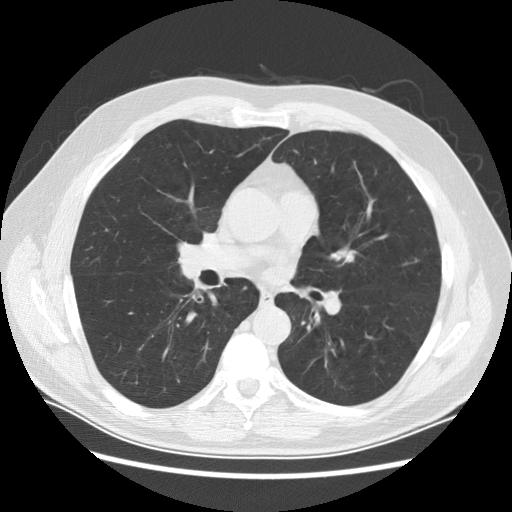
Low-dose screening chest CT, axial slice, first (baseline) screen, lung window (W 1500 / L -600 HU), 2.5 mm slice thickness, 512 × 512 image matrix. Male, age 61 years at enrolment.
Expert reader's lesion annotation, bounding box [x1, y1, x2, y2] px = [225, 276, 256, 311]. No non-calcified nodule or mass ≥4 mm was recorded by the screening reader at this exam. Later outcome: lung cancer diagnosed 756 days after this screen (after the third annual screen) — squamous cell carcinoma, keratinizing, NOS, right lower lobe, stage IIIB (AJCC 6th edition), 40 mm at pathology.